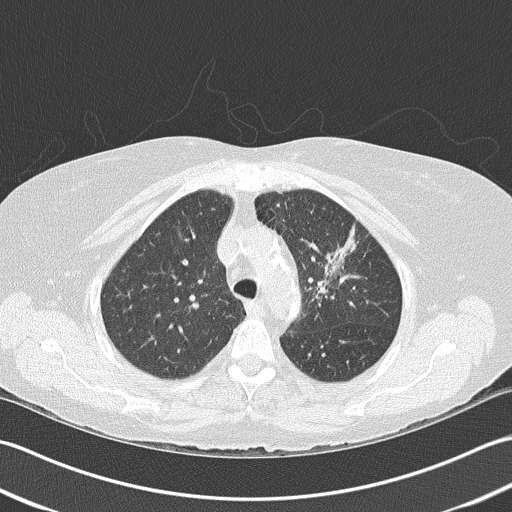
Axial slice from a low-dose chest CT screening exam, baseline screening round, lung window (W 1500 / L -600 HU), 2 mm slice thickness, lung (sharp) reconstruction kernel (B50f), slice 120 of 159 in the series, 512 × 512 image matrix, field of view 350 × 350 mm. Female, age 68 years at enrolment.
Expert reader's lesion annotation, bounding box [x1, y1, x2, y2] px = [297, 221, 372, 307]. Screening reader's record for this exam: no non-calcified nodule ≥4 mm recorded. Official screen result: negative screen, minor abnormalities not suspicious for lung cancer.